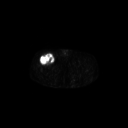
FDG PET of an extremity soft-tissue mass (from a PET/CT study), one axial slice. Slice 297 of 311 in the series (ordered by position). 3.27 mm slice thickness. 128 × 128 image matrix, field of view 700 × 700 mm. Male patient, age 56 years. From the clinical record (not read from this slice): histological type: pleiomorphic leiomyosarcoma; grade: intermediate; site of the primary tumour: right thigh.
Structures marked on this image (expert contour drawn on MRI and transferred to this co-registered scan by the dataset authors):
- gross tumour volume including surrounding oedema: box from (x=40, y=52) to (x=55, y=65) px
- gross tumour volume (mass): (x=40, y=53)–(x=55, y=65)